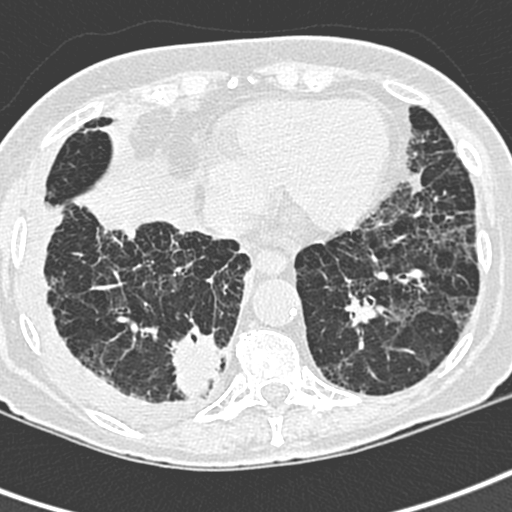
Low-dose screening chest CT, one axial slice. Slice 83 of 220 in the series (ordered by position). Lung window (W 1500 / L -600 HU). 512 × 512 image matrix.
Structures marked on this image (manually delineated by an expert):
- lesion 1 (tumor, lower lobe of right lung): bounding box <171,326,225,400> (left, top, right, bottom; pixels)